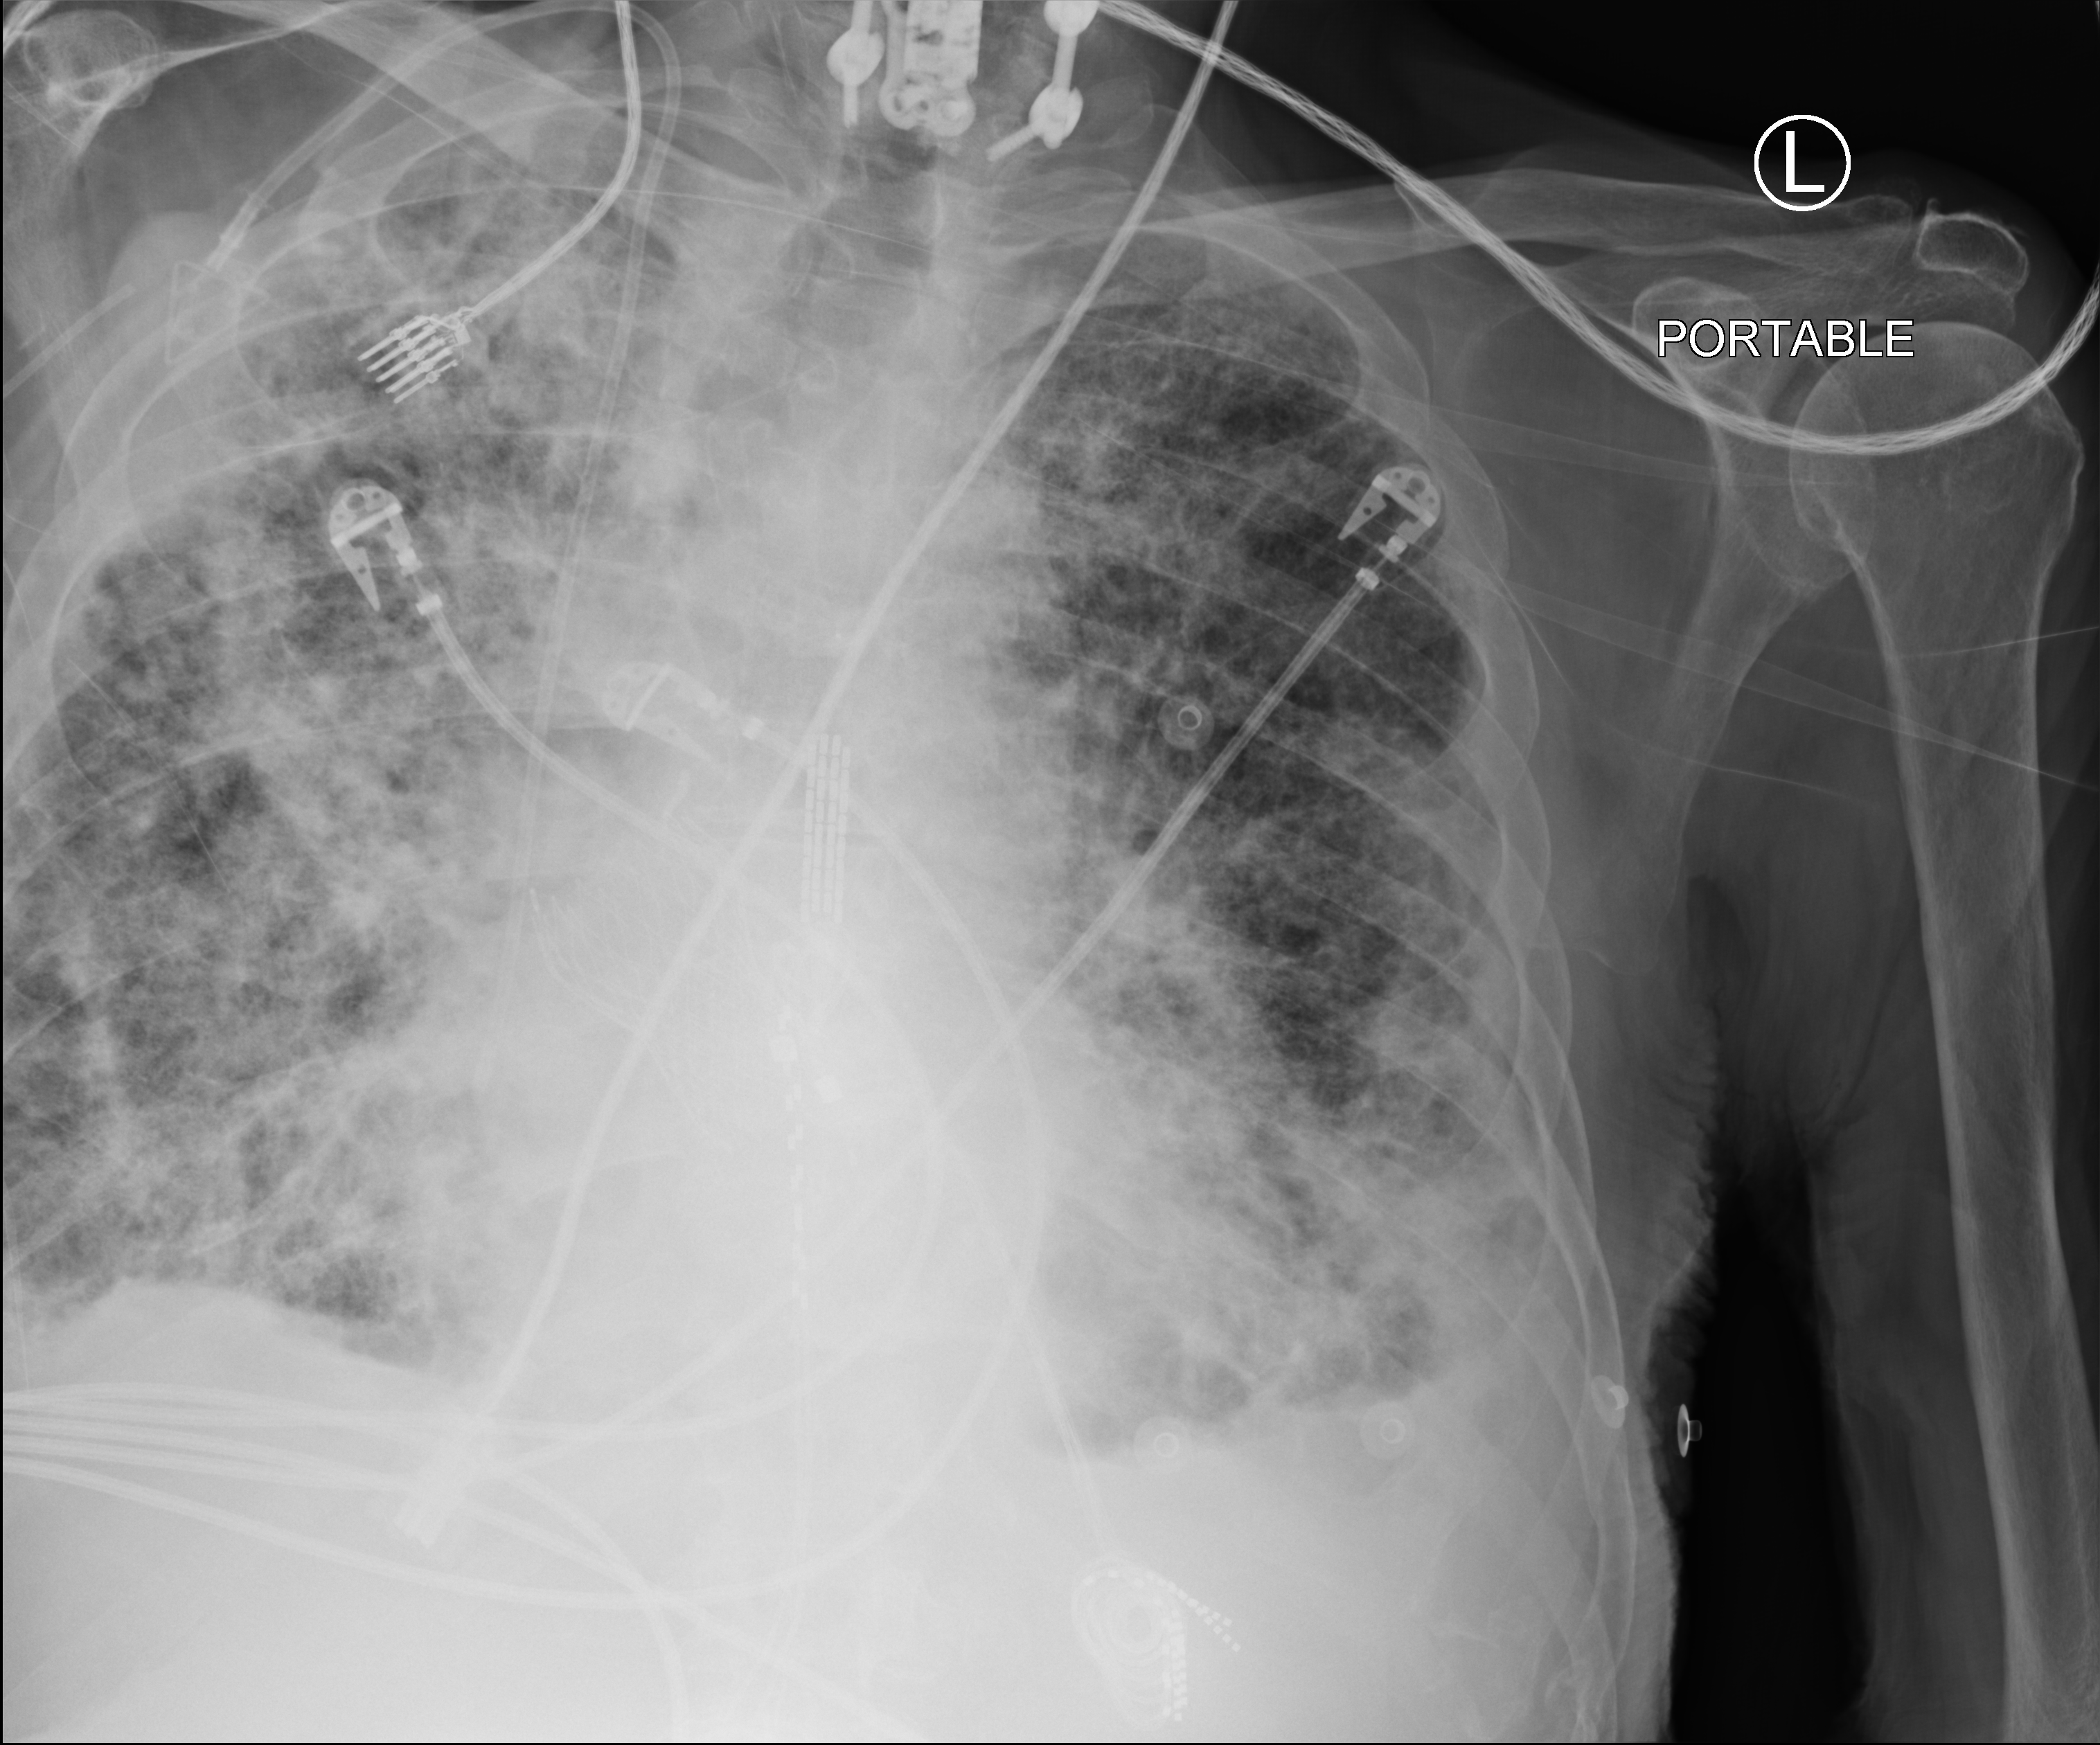
Chest X-ray (portable). Patient hospitalised with COVID-19; male, aged 75–90 years.
From the hospital-stay record, not from the radiograph (when in the stay this image was taken is not recorded):
- admitted to intensive care during this hospital stay: yes
- diabetes (admission record): no
- mechanically ventilated during this hospital stay: no